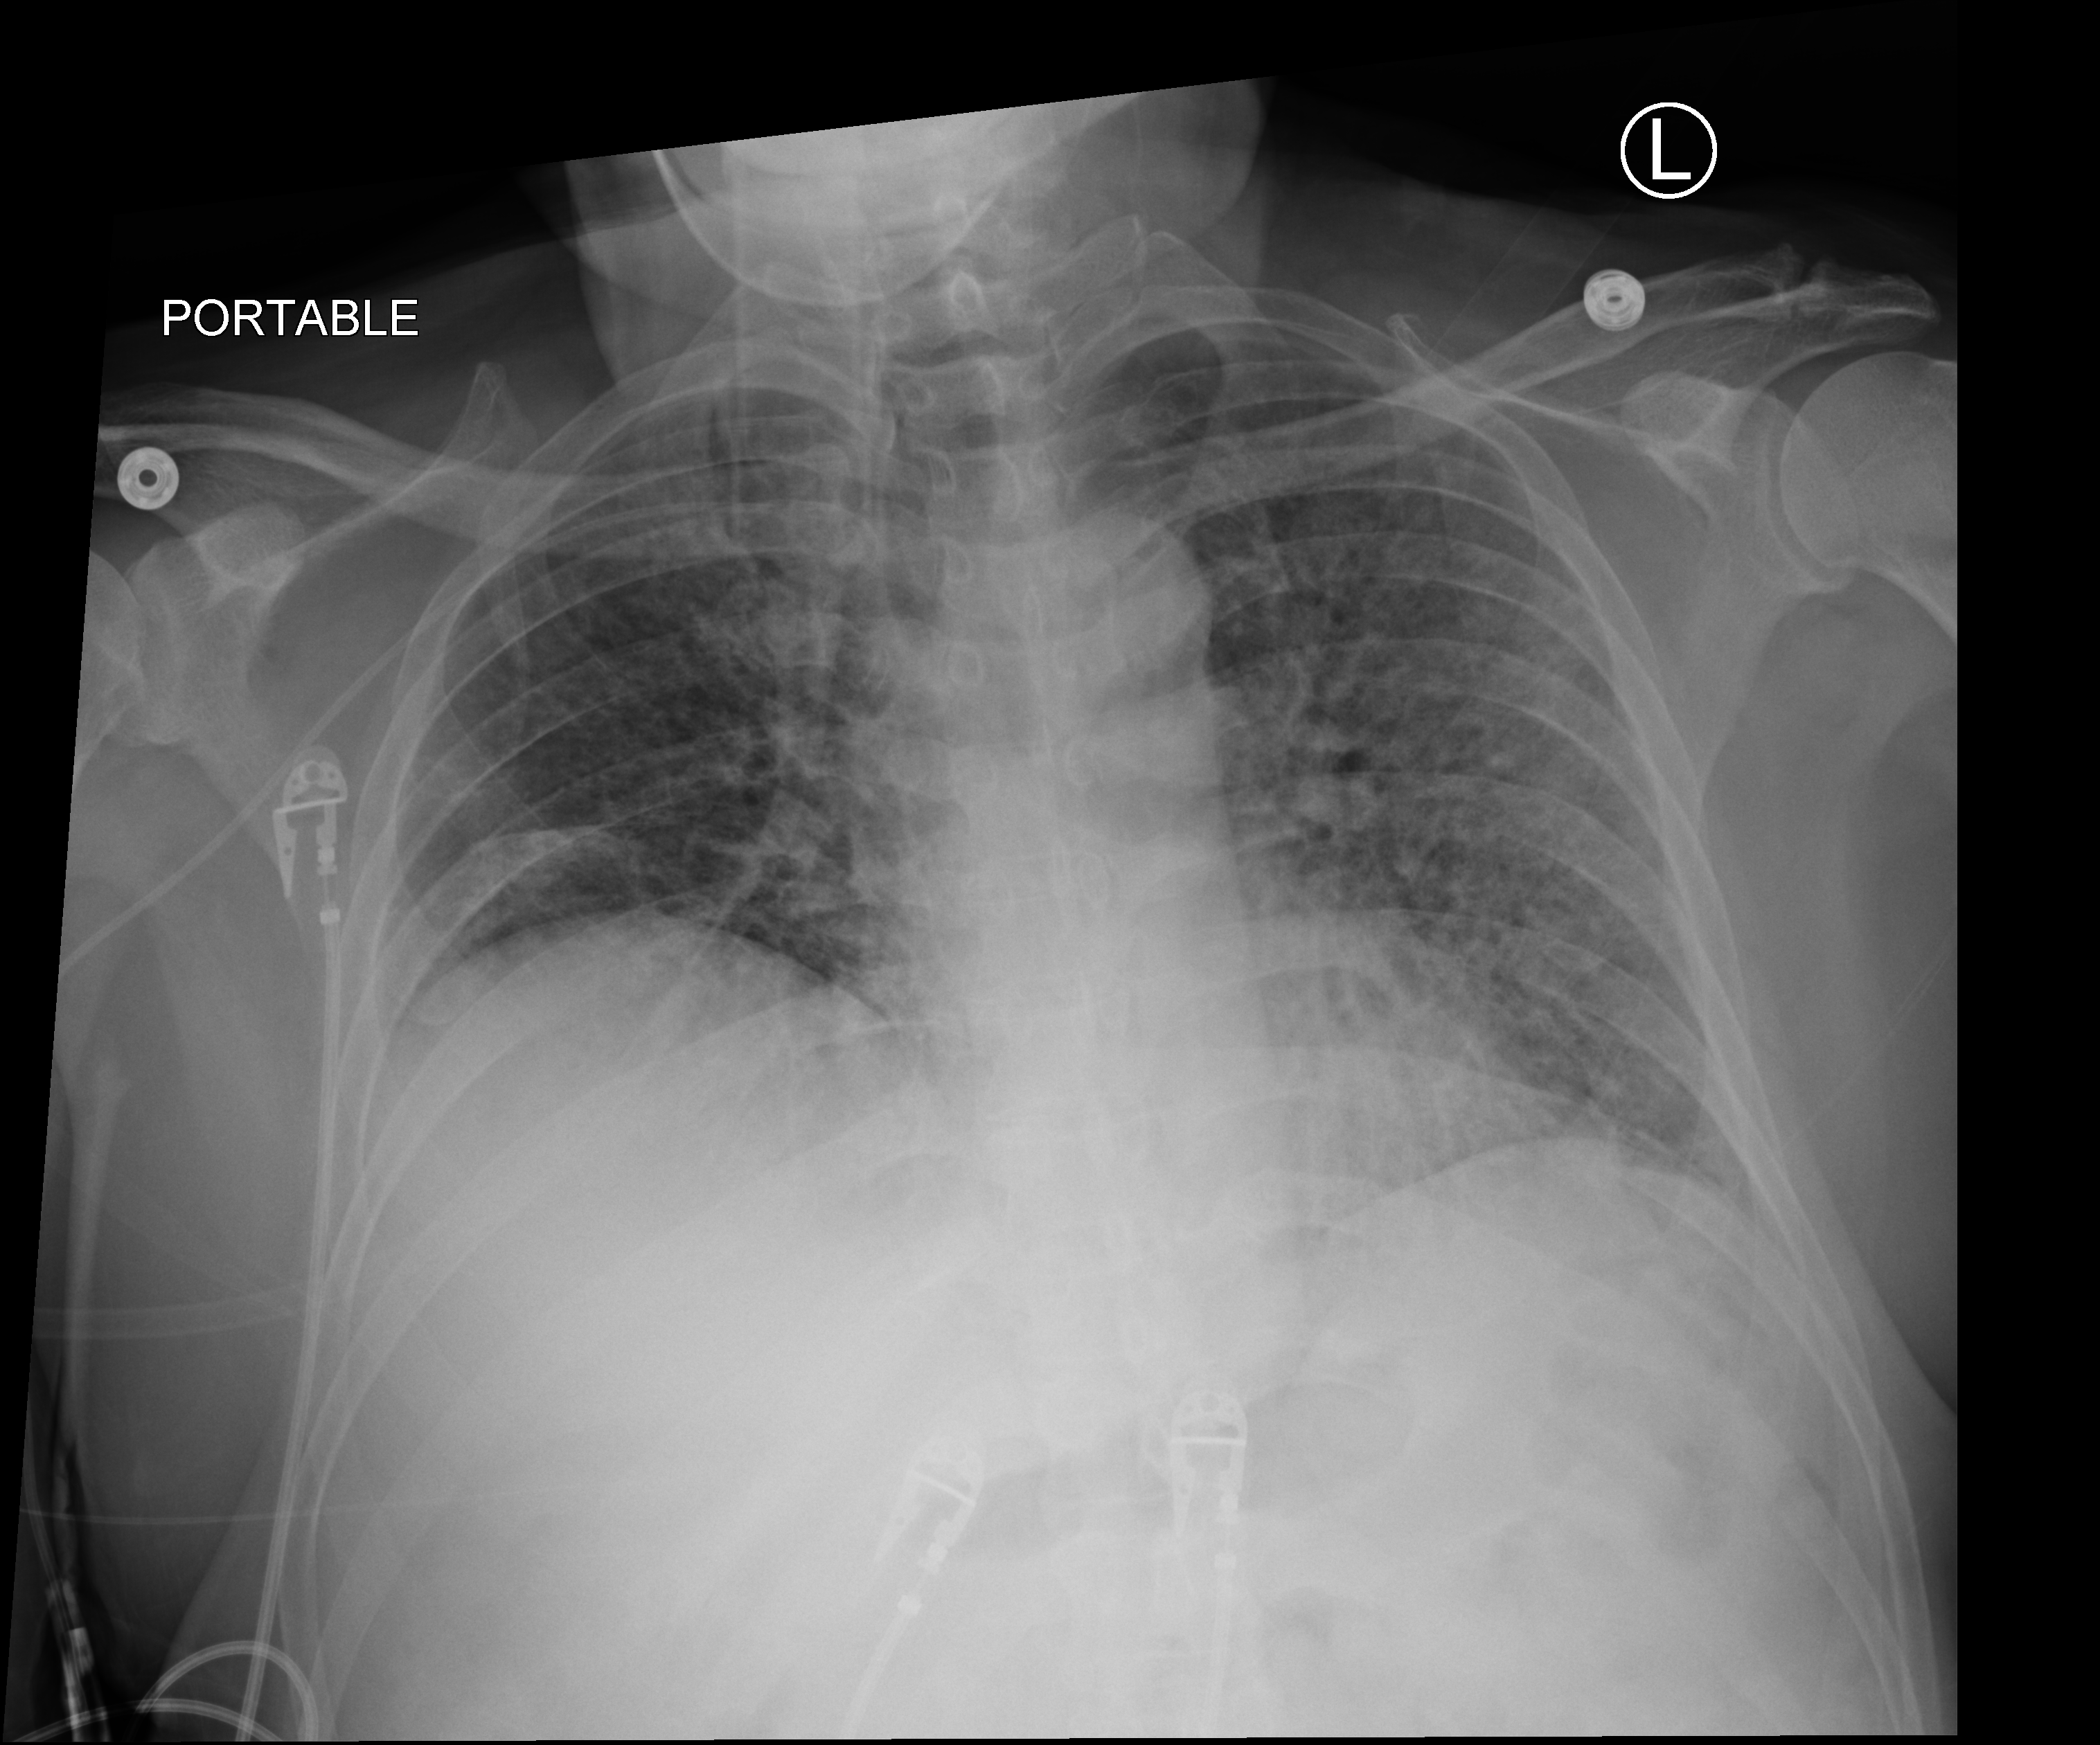
Bedside chest radiograph (computed radiography). Male patient hospitalised with COVID-19, age 18–59 years.
Hospital-stay facts (about this admission, not read from this image; timing relative to this image not recorded):
- admitted to intensive care during this hospital stay: yes